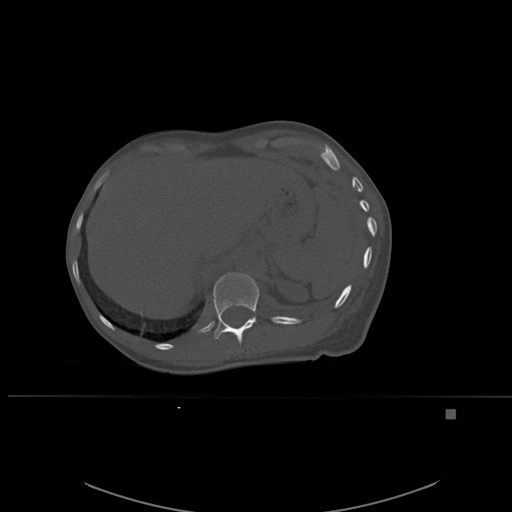
CT including the spine, one axial slice; position 280 of 537 along the scan axis; bone window (W 1800 / L 400 HU); 1.5 mm slice thickness; 512 × 512 image matrix, field of view 440 × 440 mm. Female patient, age 45 years. Case-level facts recorded for this patient, not image findings: primary cancer: lung.
Structures marked on this image (semi-automatically segmented with operator editing):
- T12 vertebra: bounding box [x1, y1, x2, y2] px = [213, 272, 260, 344]